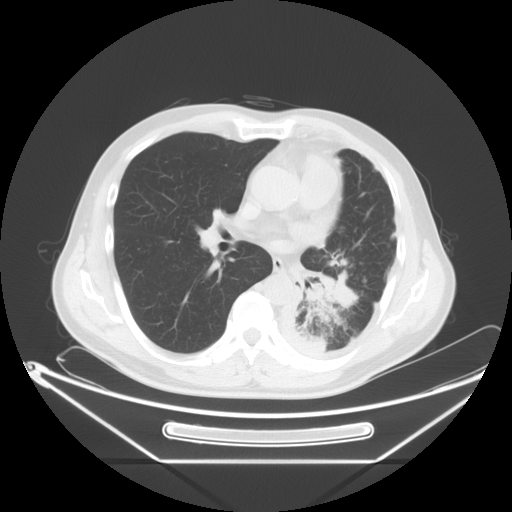
Chest CT, one axial slice. Position 33 of 63 along the scan axis. 120 kVp. Lung window (W 1500 / L -600 HU). 5 mm slice thickness. 512 × 512 image matrix, field of view 442 × 442 mm. Male patient, age 60 years. From the clinical record (not read from this slice): clinical TNM (as recorded): T4 N1 M1.
Structures marked on this image (rectangle marked by the reading radiologist):
- lung tumour (recorded histology: adenocarcinoma): bounding box (x1, y1, x2, y2) in pixels: (292, 262, 362, 342)